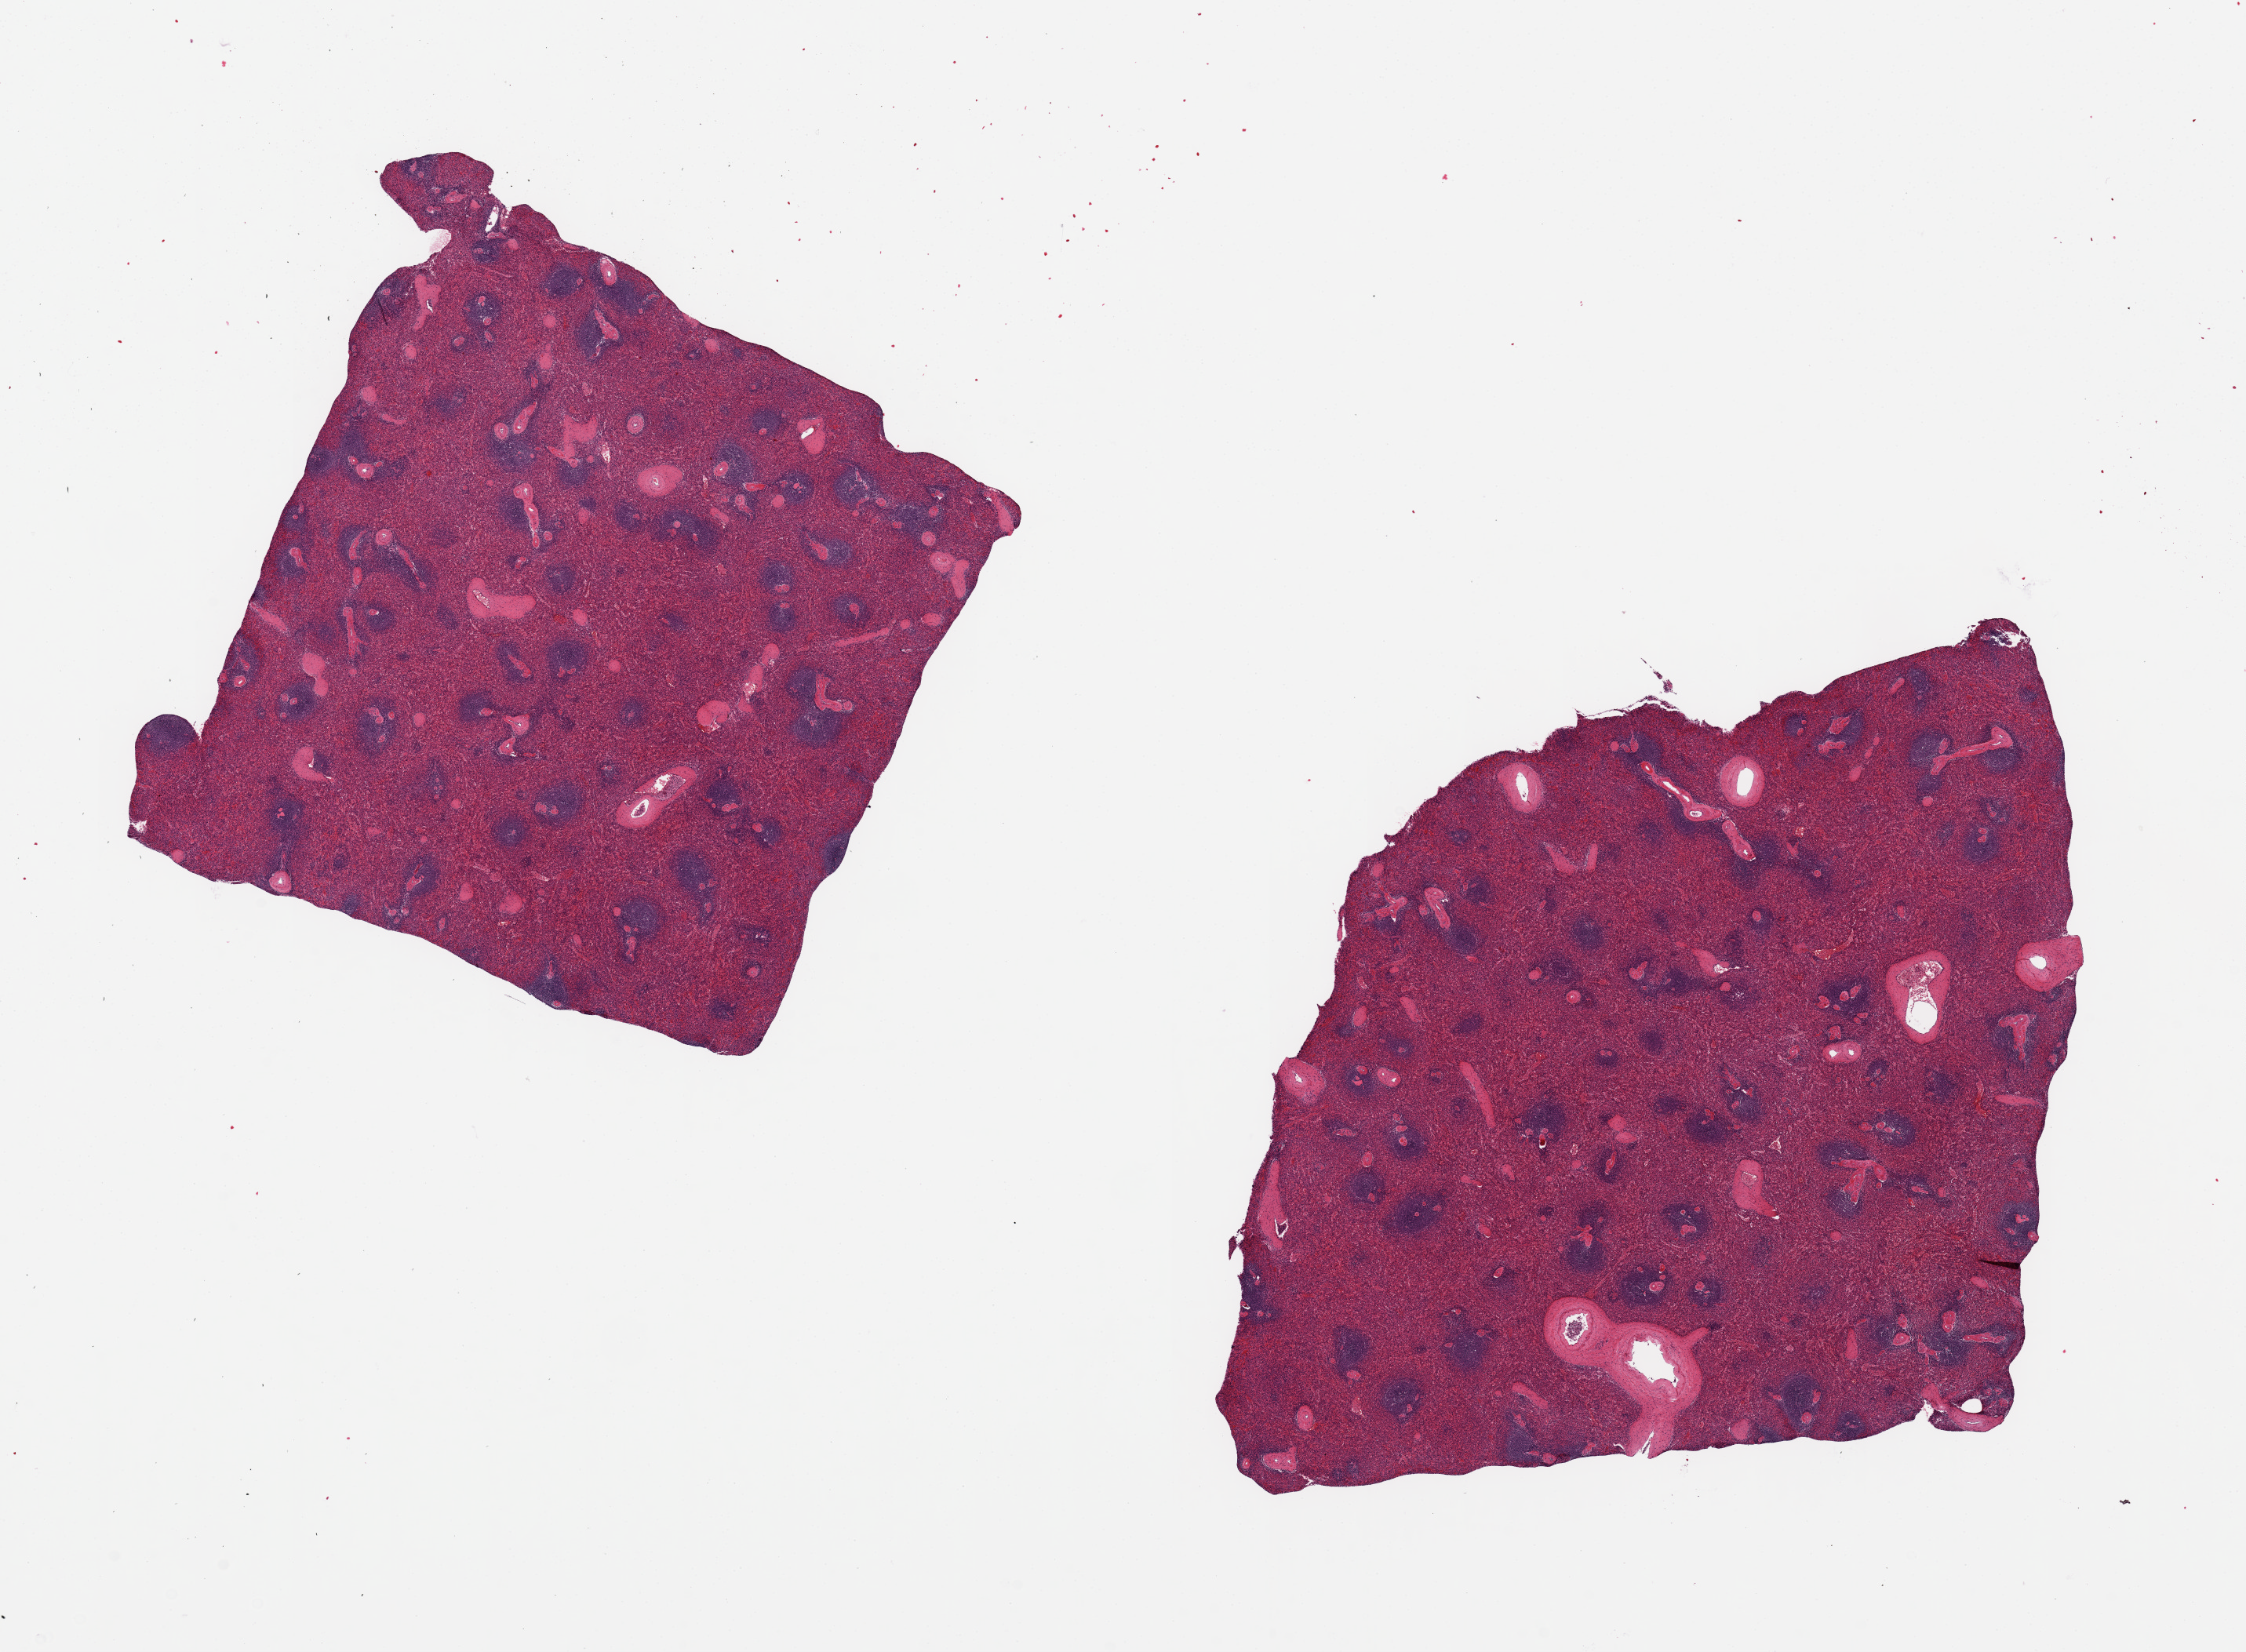
Whole-slide image, haematoxylin and eosin stain, shown as a low-resolution overview of the whole scanned area (about 22.6 x 16.7 mm), PAXgene-fixed, paraffin-embedded tissue, target tissue: spleen, donor tissue sample. Donor: male.
Review note (as recorded): 2 pieces, ~8x8mm, moderate congestion.